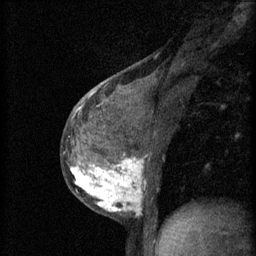
Breast MRI (dynamic contrast-enhanced), one sagittal slice; position 30 of 60 along the scan axis; 3 images stored at this slice position (order not interpretable as contrast timing); 1.5 T; TE 4.2 ms, TR 11 ms; 2 mm slice thickness; 256 × 256 image matrix, field of view 180 × 180 mm. Female patient, age 37 years.
Annotated regions visible in this slice (semi-automatic segmentation, software-assisted and operator-edited):
- analysis volume of interest (the breast-tissue region the enhancement analysis was run in; not a lesion): box from (x=65, y=138) to (x=152, y=219) px
- tumour enhancement mask (voxels above the 70 % enhancement threshold inside the analysis volume of interest): (x=70, y=154)–(x=144, y=215)